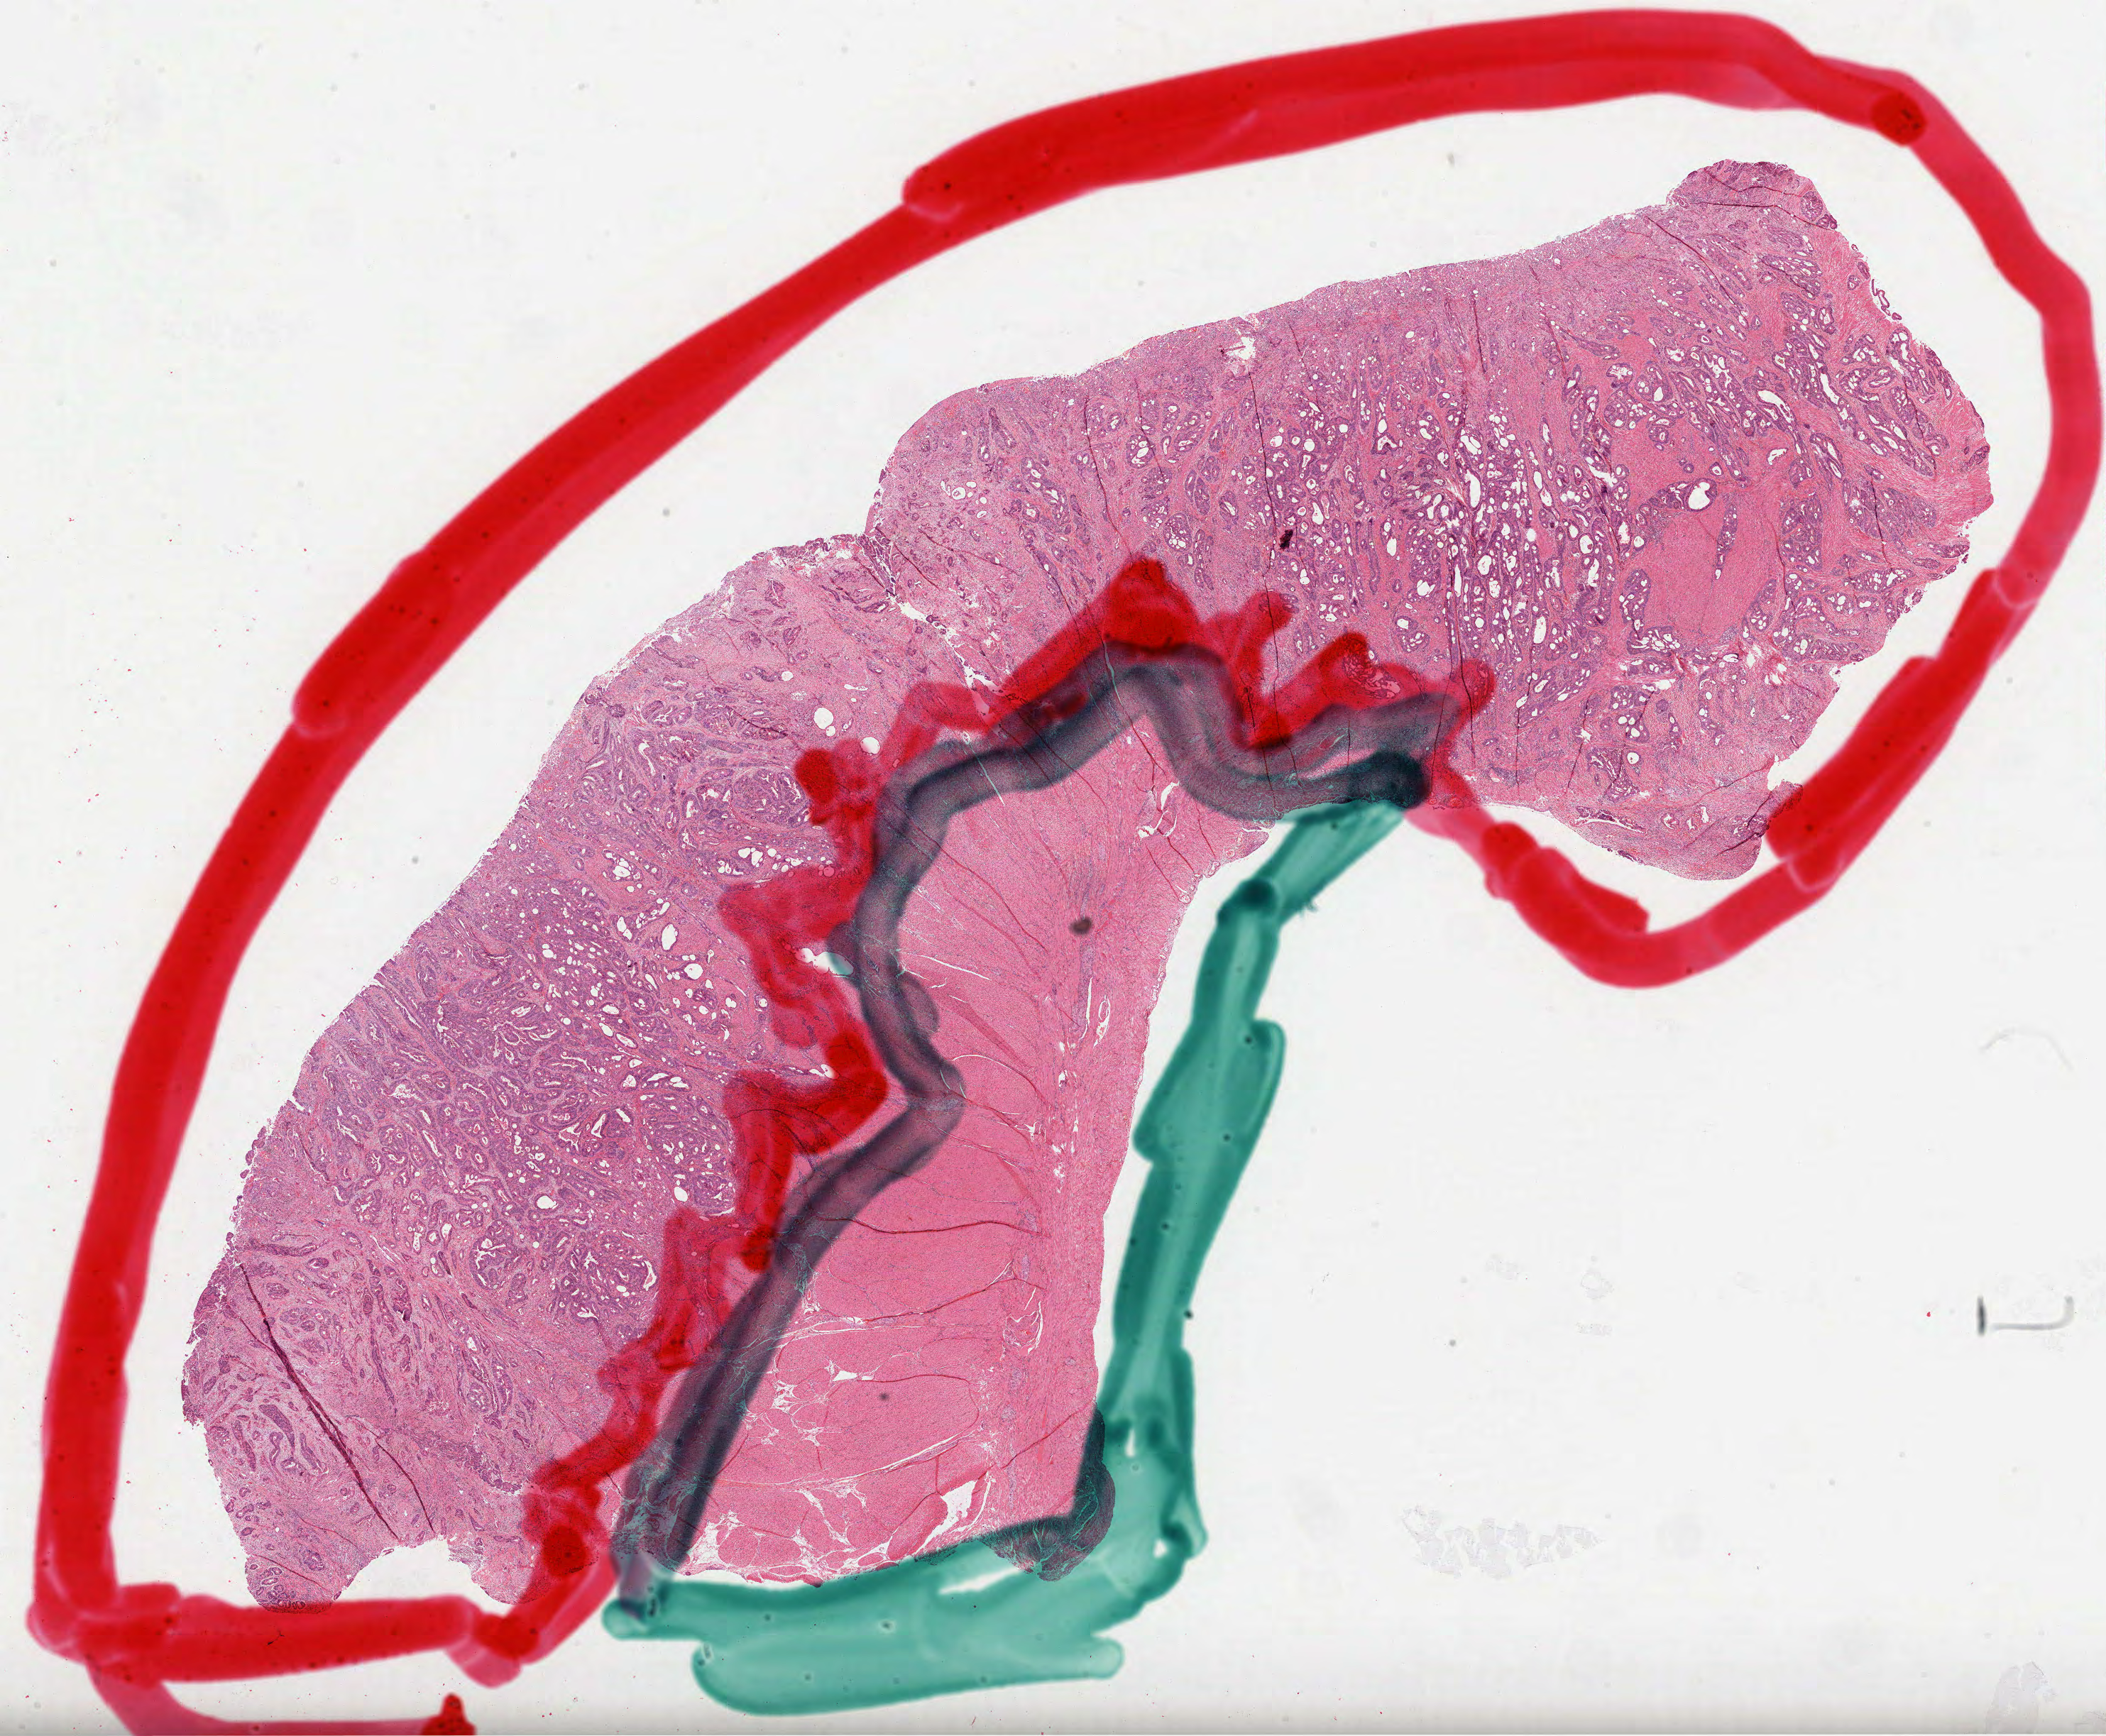
Whole-slide histology image, H&E — low-resolution overview of the scanned area, about 23.9 x 19.7 mm. FFPE section. Stomach, primary tumour sample. Patient: male, age at initial diagnosis 70 years. Histologic grade: G2 (moderately differentiated).
* TNM: T3 N0 M0
* AJCC pathologic stage: IIA (7th edition)
* pathologic diagnosis: Adenocarcinoma, NOS
* lymph nodes positive (case pathology): 0 of 8 examined